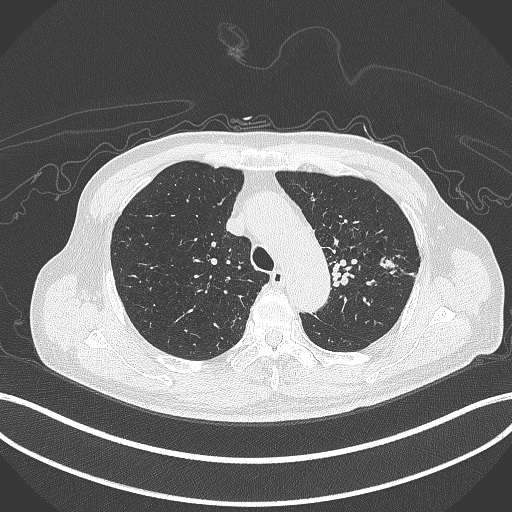
Chest CT, one axial slice; position 329 of 417 along the scan axis; lung window (W 1500 / L -600 HU); 1 mm slice thickness; 512 × 512 image matrix, field of view 400 × 400 mm. Patient: male, 77 years. From the clinical record (not read from this slice): clinical TNM (as recorded): T3 N1 M0.
Structures marked on this image (bounding box drawn by a radiologist):
- lung tumour (recorded histology: adenocarcinoma): box from (x=379, y=253) to (x=400, y=272) px